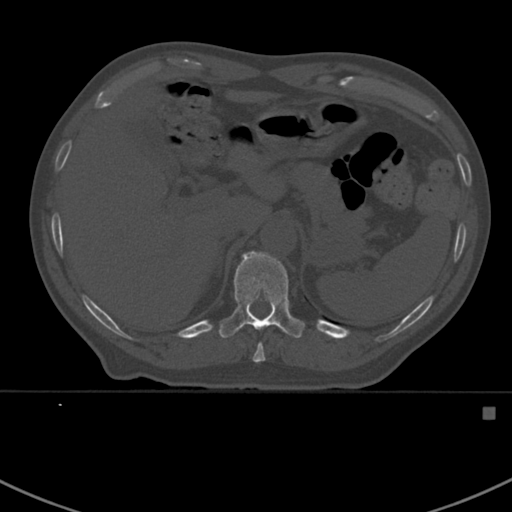
CT including the spine, one axial slice; position 351 of 412 along the scan axis; 120 kVp; bone window (W 1800 / L 400 HU); 1.5 mm slice thickness; 512 × 512 image matrix. Male patient, age 59 years. From the clinical record (not read from this slice): primary cancer: prostate.
Structures marked on this image (semi-automatically segmented with operator editing):
- T10 vertebra: bounding box (x1, y1, x2, y2) in pixels: (253, 343, 265, 363)
- T11 vertebra: (219, 251, 305, 338)